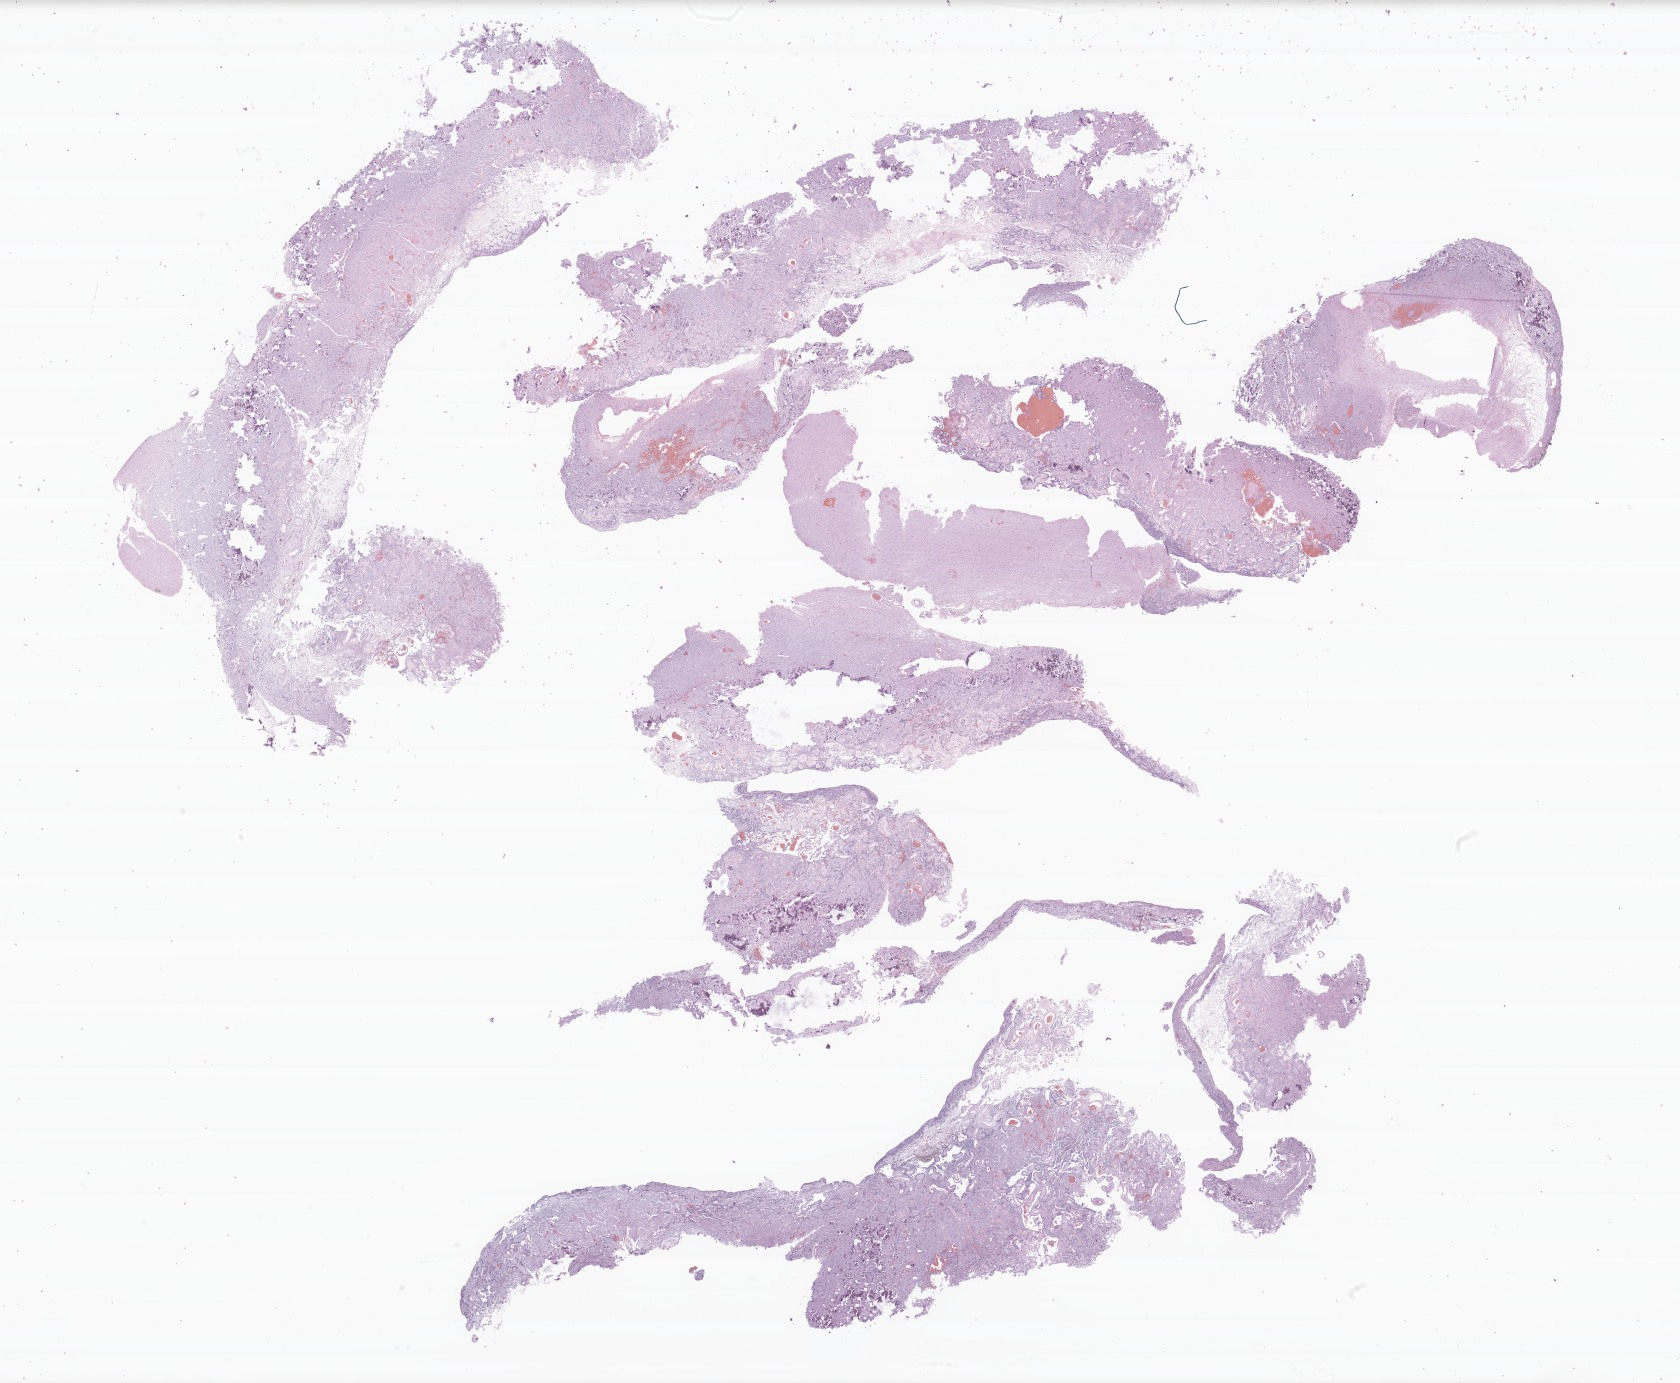
Hematoxylin and eosin (H&E) whole-slide image of tumor tissue from the brain, shown as a low-resolution overview of the whole scanned area (about 28.3 x 23.3 mm); formalin-fixed, paraffin-embedded (FFPE) tissue. Male patient, age 215 months (17 years 11 months).
Recorded diagnosis: Tumor cells, benign.